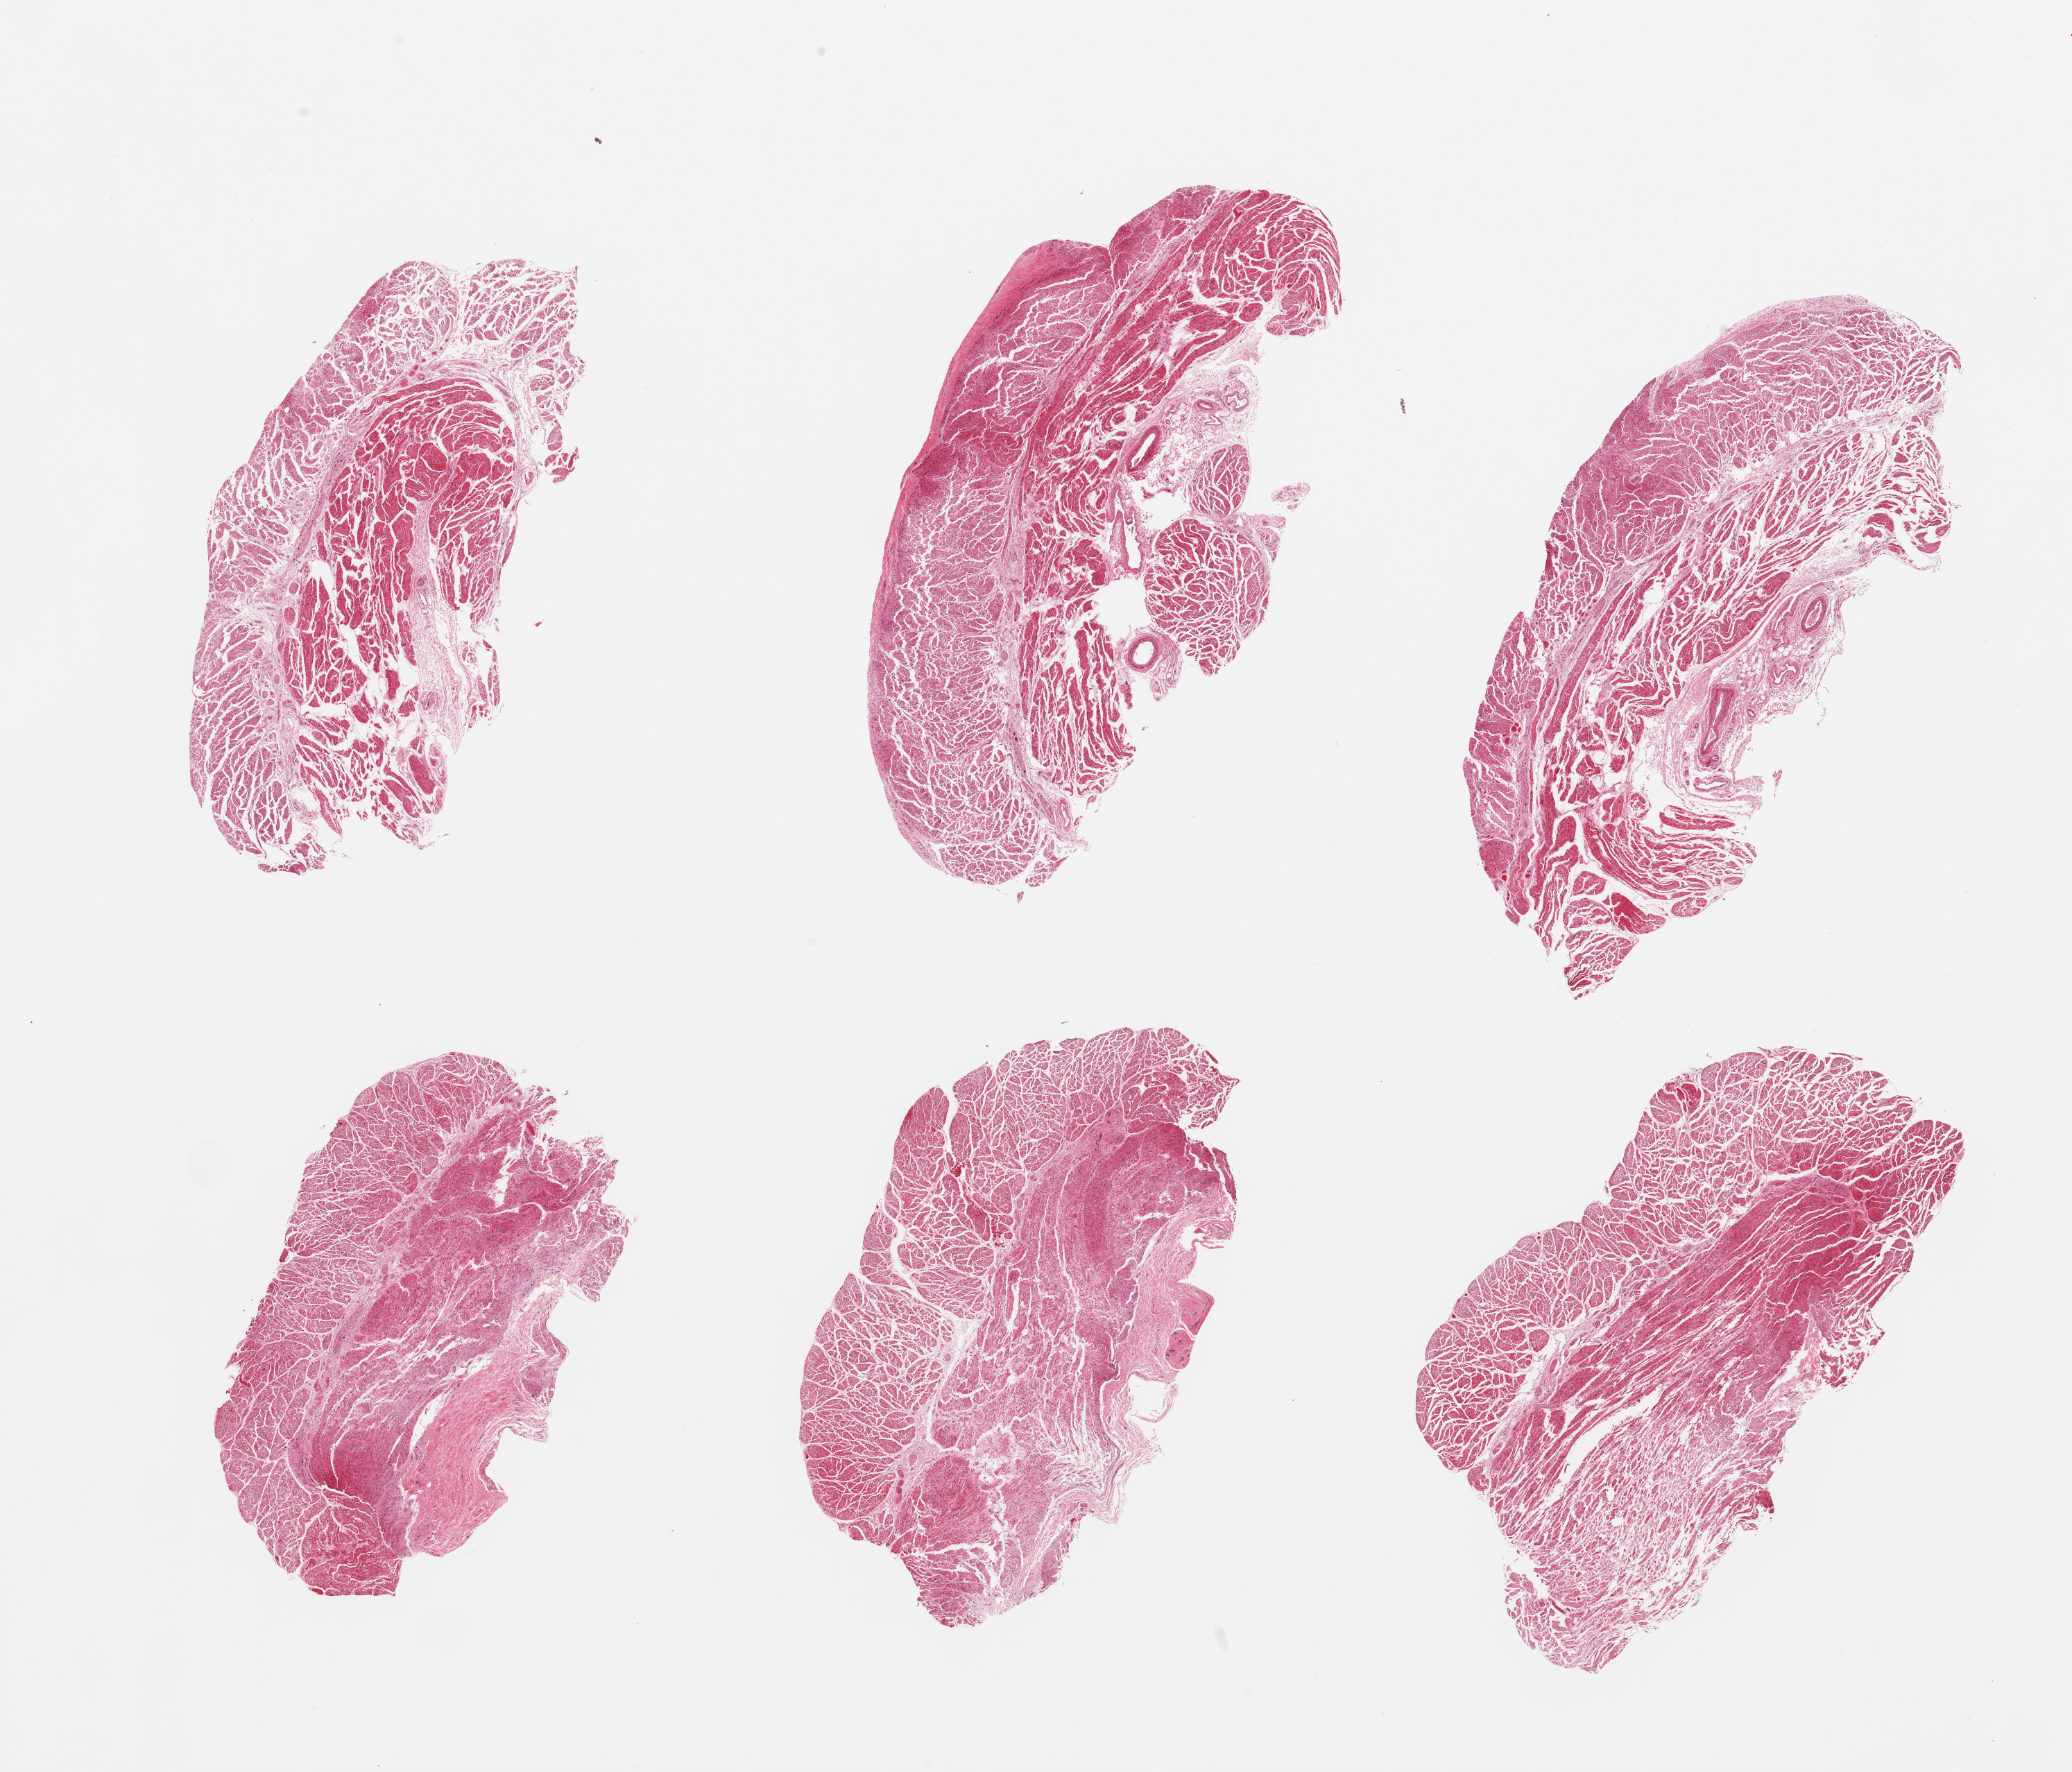
Whole-slide image, hematoxylin and eosin (H&E) stain — shown as a low-resolution overview of the whole scanned area (about 23.6 x 20.2 mm). PAXgene-fixed, paraffin-embedded tissue. Sampled site (target tissue): esophageal muscle. Tissue donor sample. Male donor.
Review note (as recorded): 6 pieces; well trimmed.